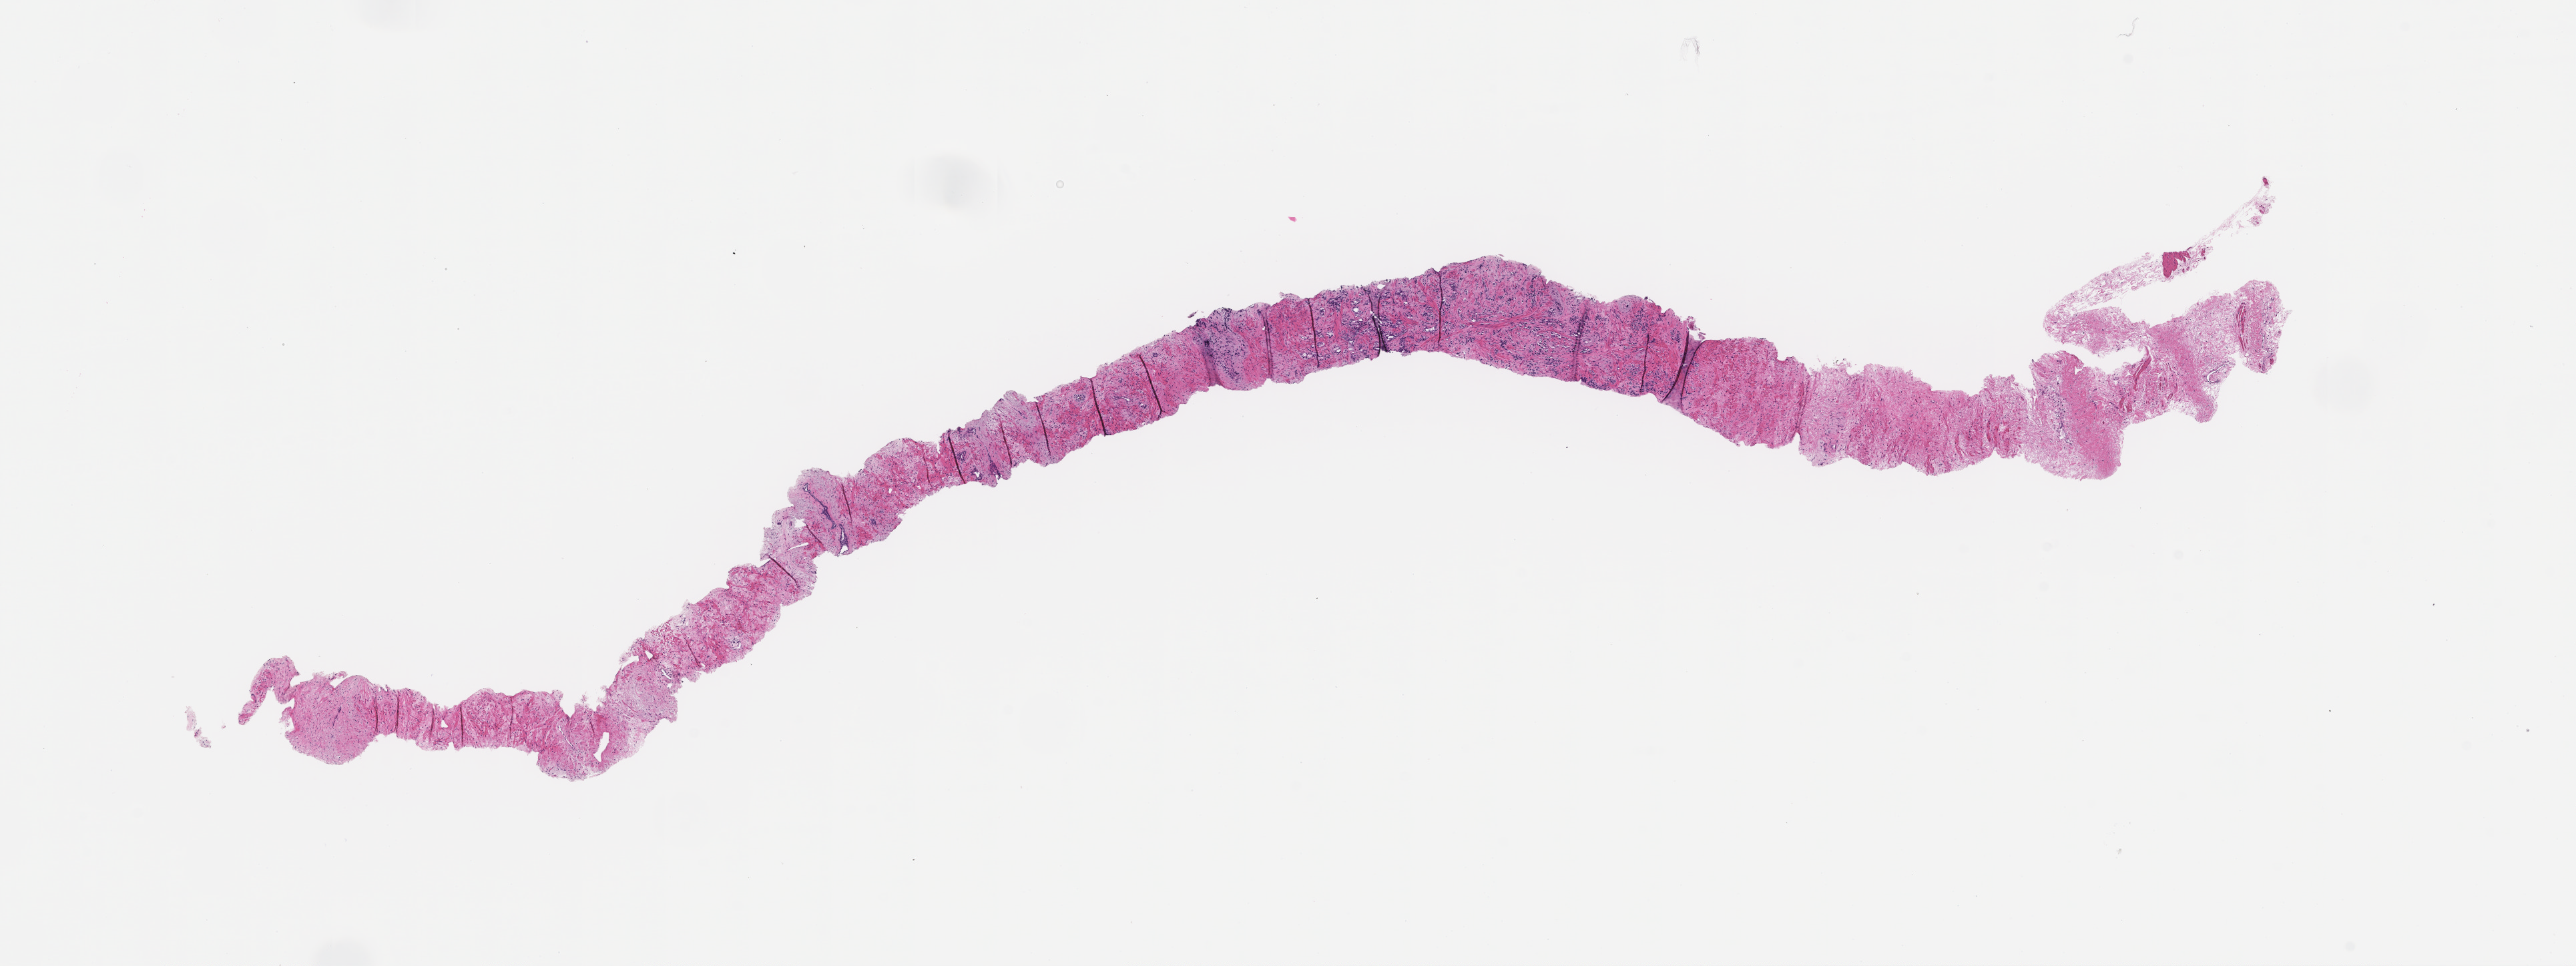
Hematoxylin and eosin (H&E) whole-slide image, whole scanned area (about 15.6 x 5.8 mm) shown as a low-resolution overview, formalin-fixed paraffin-embedded section, tissue site: prostate, specimen time point: archival tissue. Patient: male.
* this section: primary tumour tissue
* diagnosis: Prostate Carcinoma